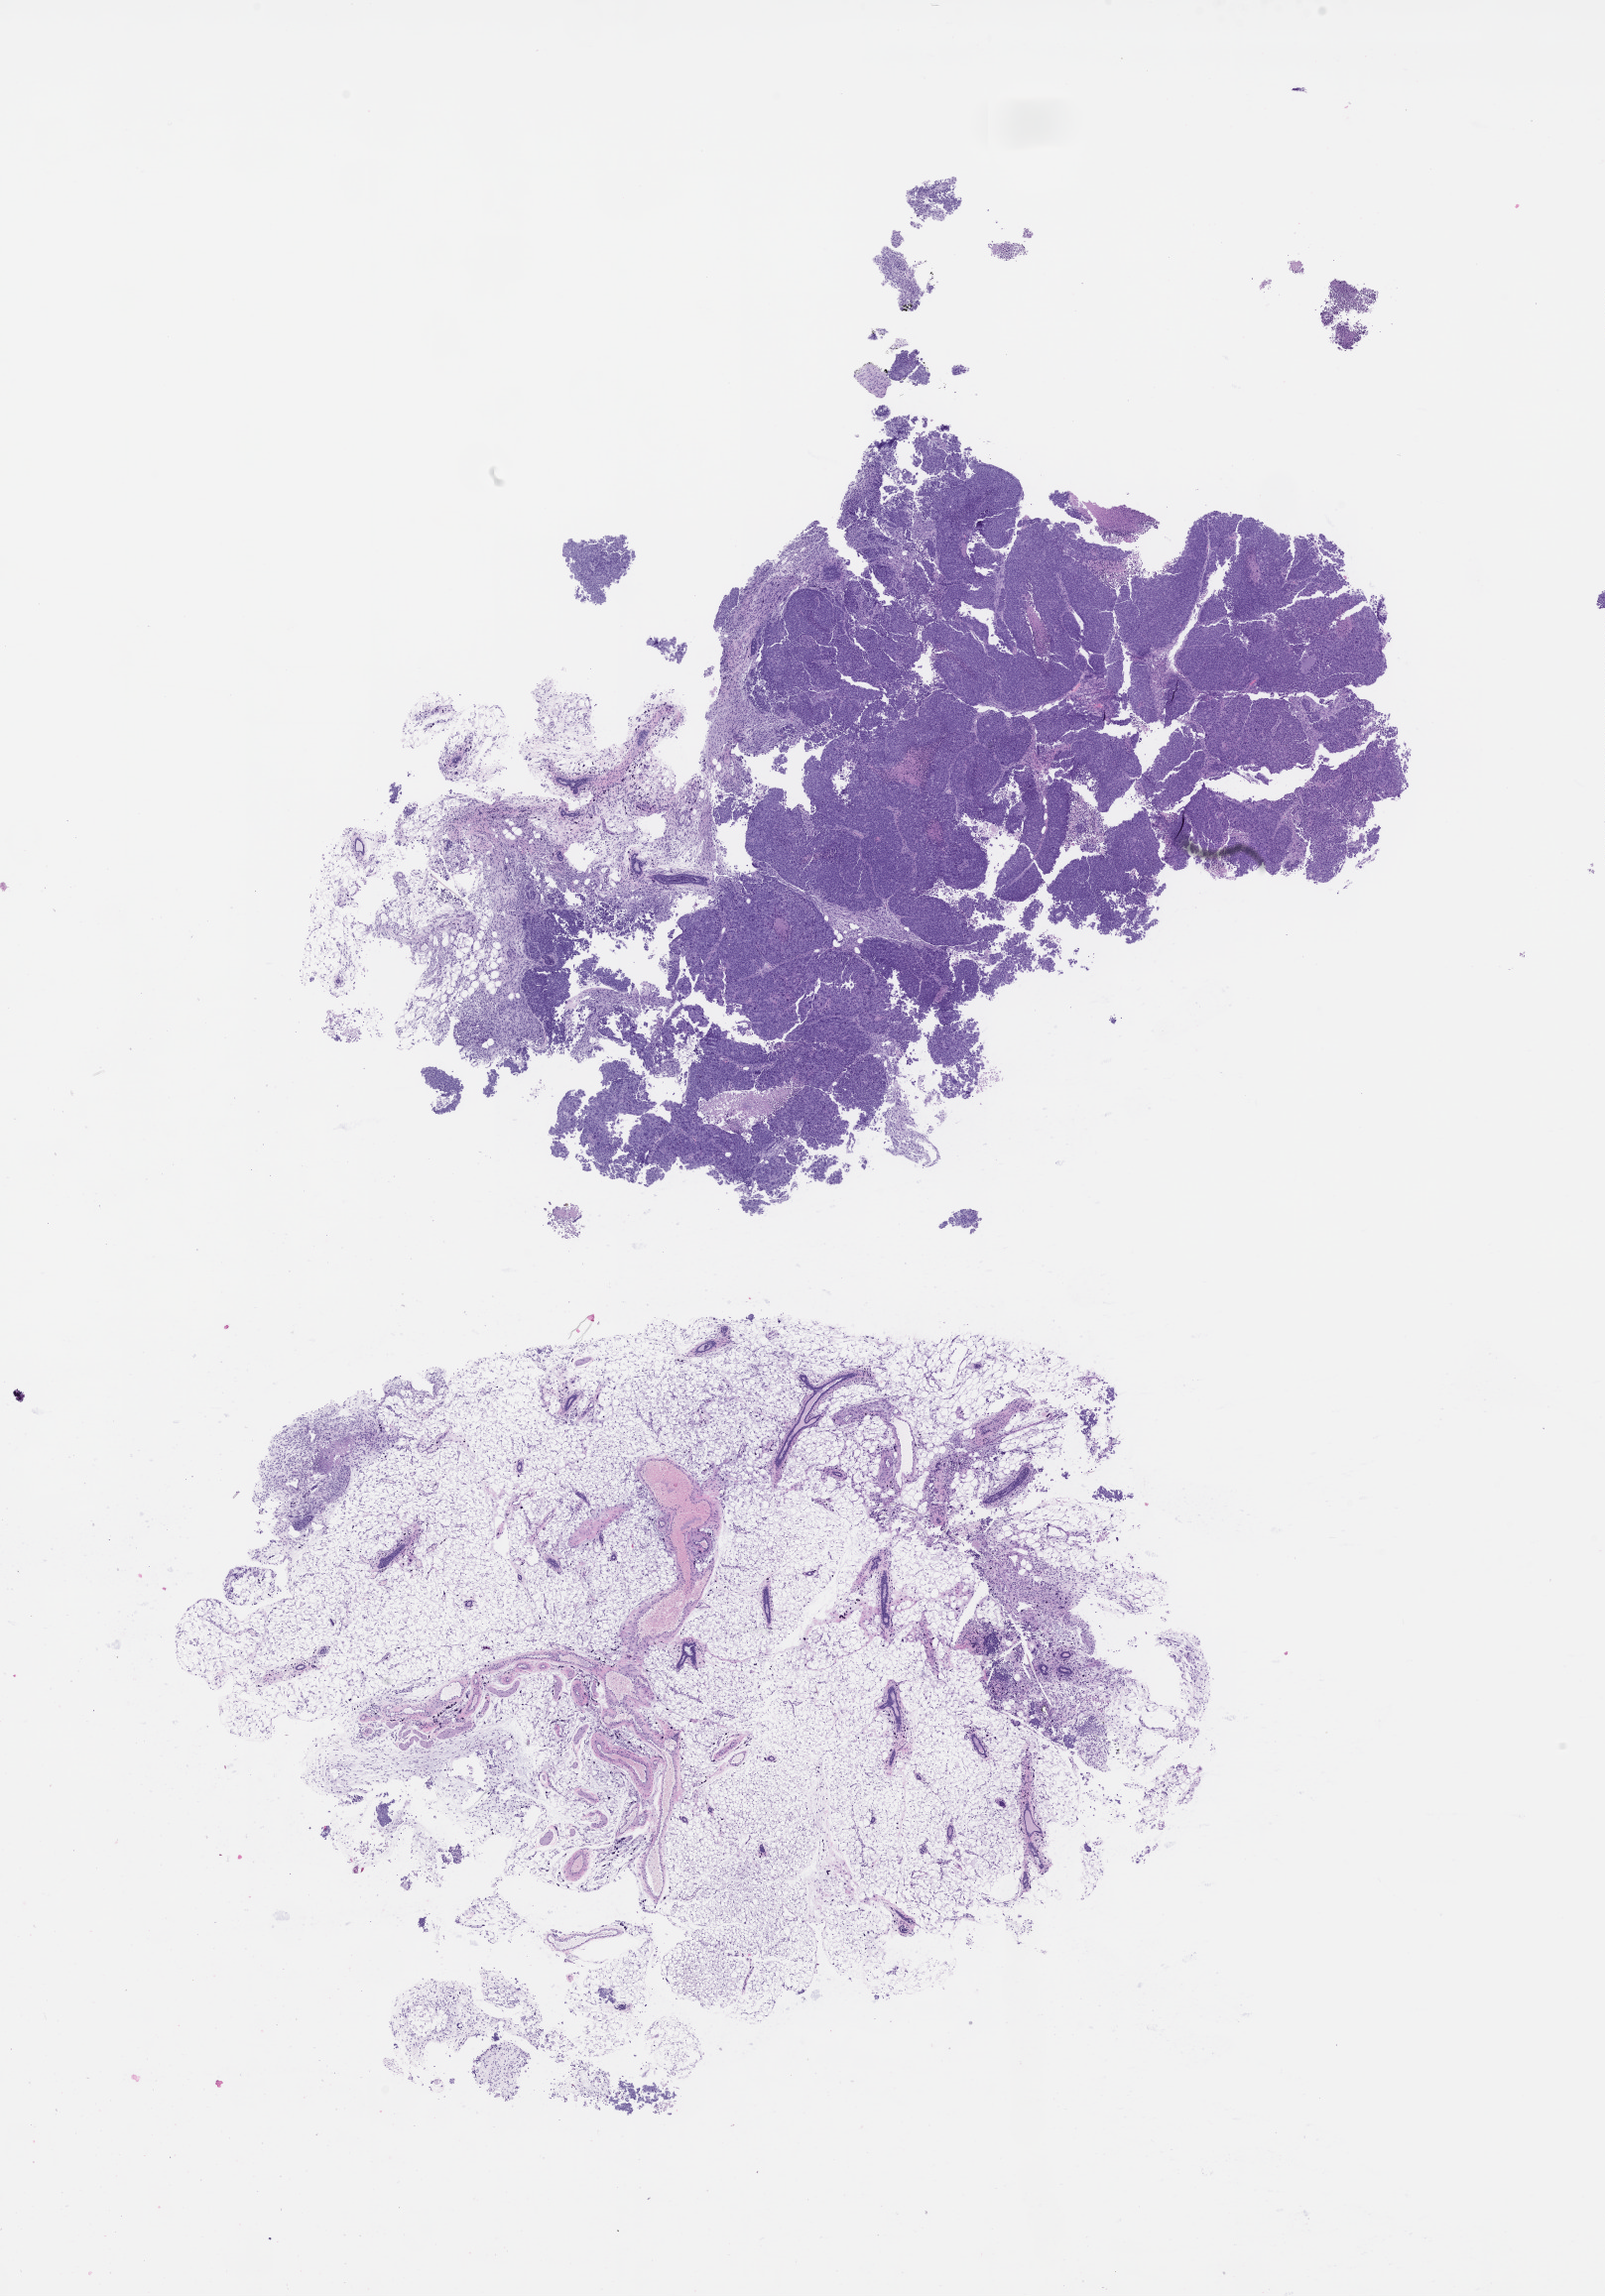
Hematoxylin and eosin (H&E) whole-slide image of a patient-derived xenograft (PDX) tumor grown in a mouse, passage 2, a low-resolution overview of the entire scanned area, about 13.0 x 18.5 mm. FFPE section. Originating tumor site category: lung.
Originating patient diagnosis: Lung Squamous Cell Carcinoma.